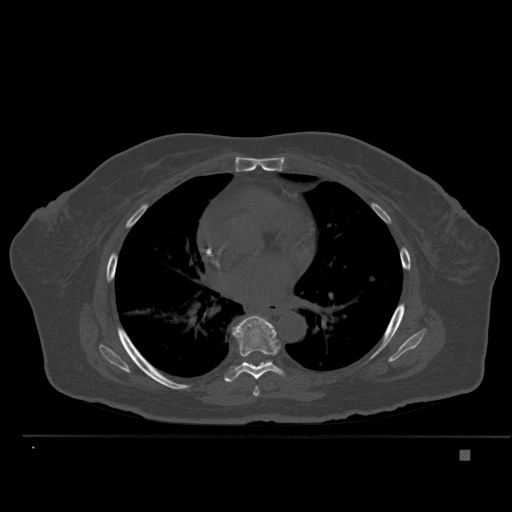
CT including the spine, one axial slice. Position 325 of 477 along the scan axis. Bone window (W 1800 / L 400 HU). 1.5 mm slice thickness. 512 × 512 image matrix. Patient: female, 74 years. From the clinical record (not read from this slice): primary cancer: colon.
Annotated regions visible in this slice (semi-automatic segmentation, software-assisted and operator-edited):
- T6 vertebra: bounding box (x1, y1, x2, y2) in pixels: (253, 387, 260, 397)
- T7 vertebra: (224, 315, 284, 382)
- T8 vertebra: (266, 360, 273, 363)